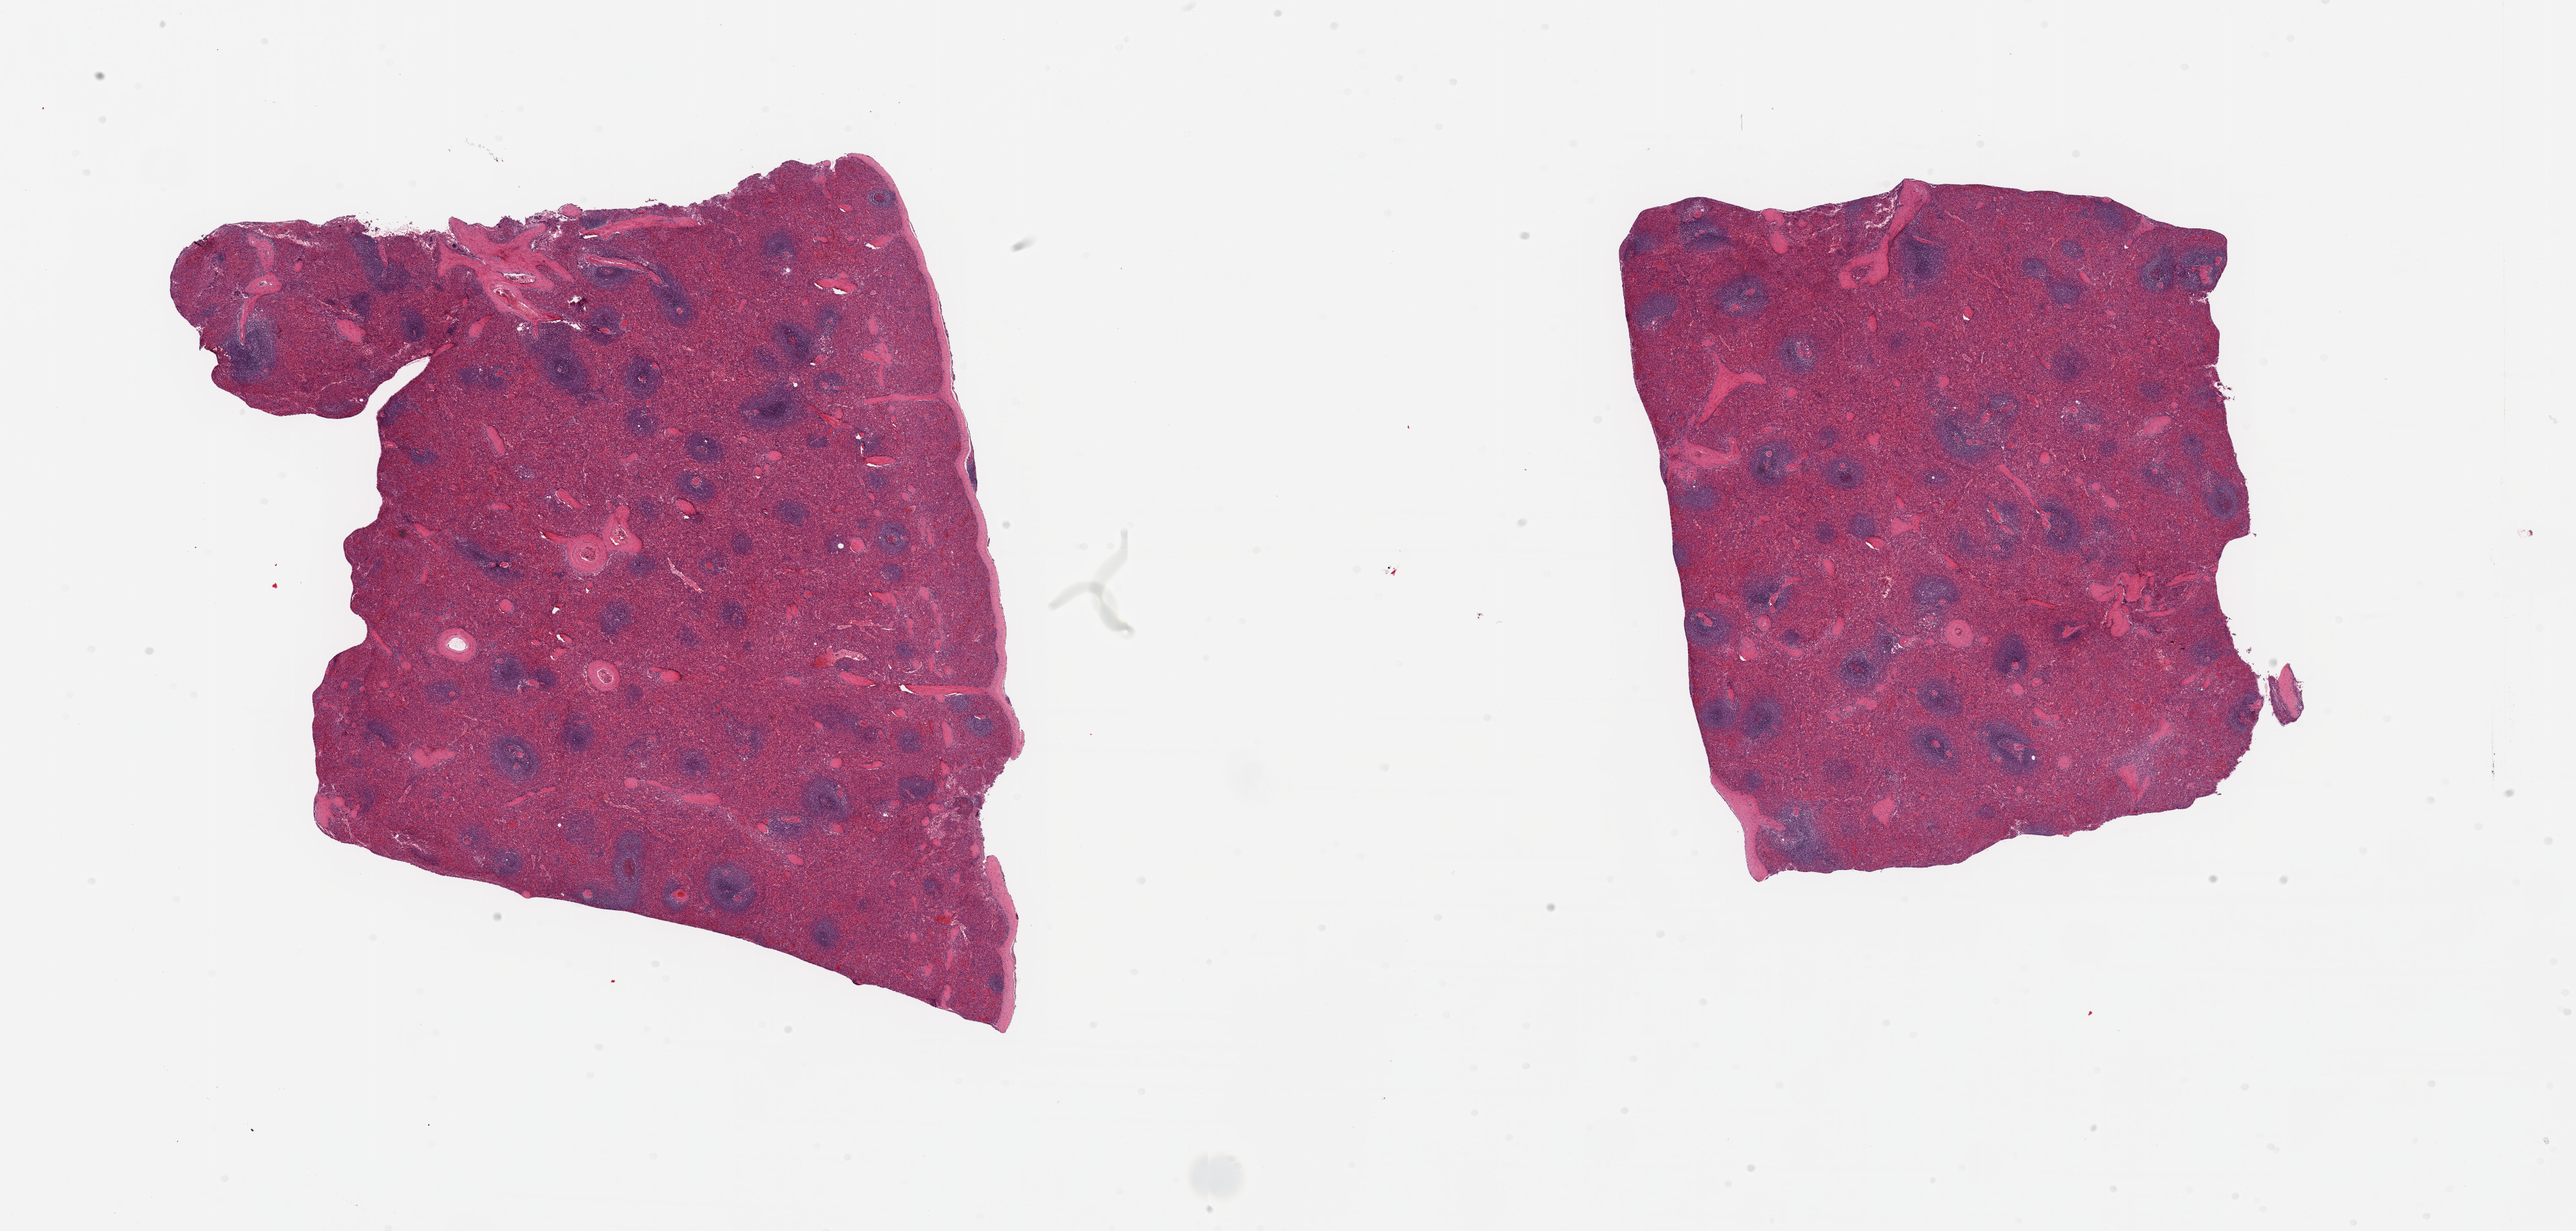
Whole-slide image, hematoxylin and eosin (H&E) stain — low-resolution overview of the scanned area, about 31.5 x 15.1 mm, PAXgene-fixed, paraffin-embedded tissue, target tissue: spleen, tissue donor sample. Donor: male.
Pathologist's review note for this sample: 2 pieces, no abnormalities.